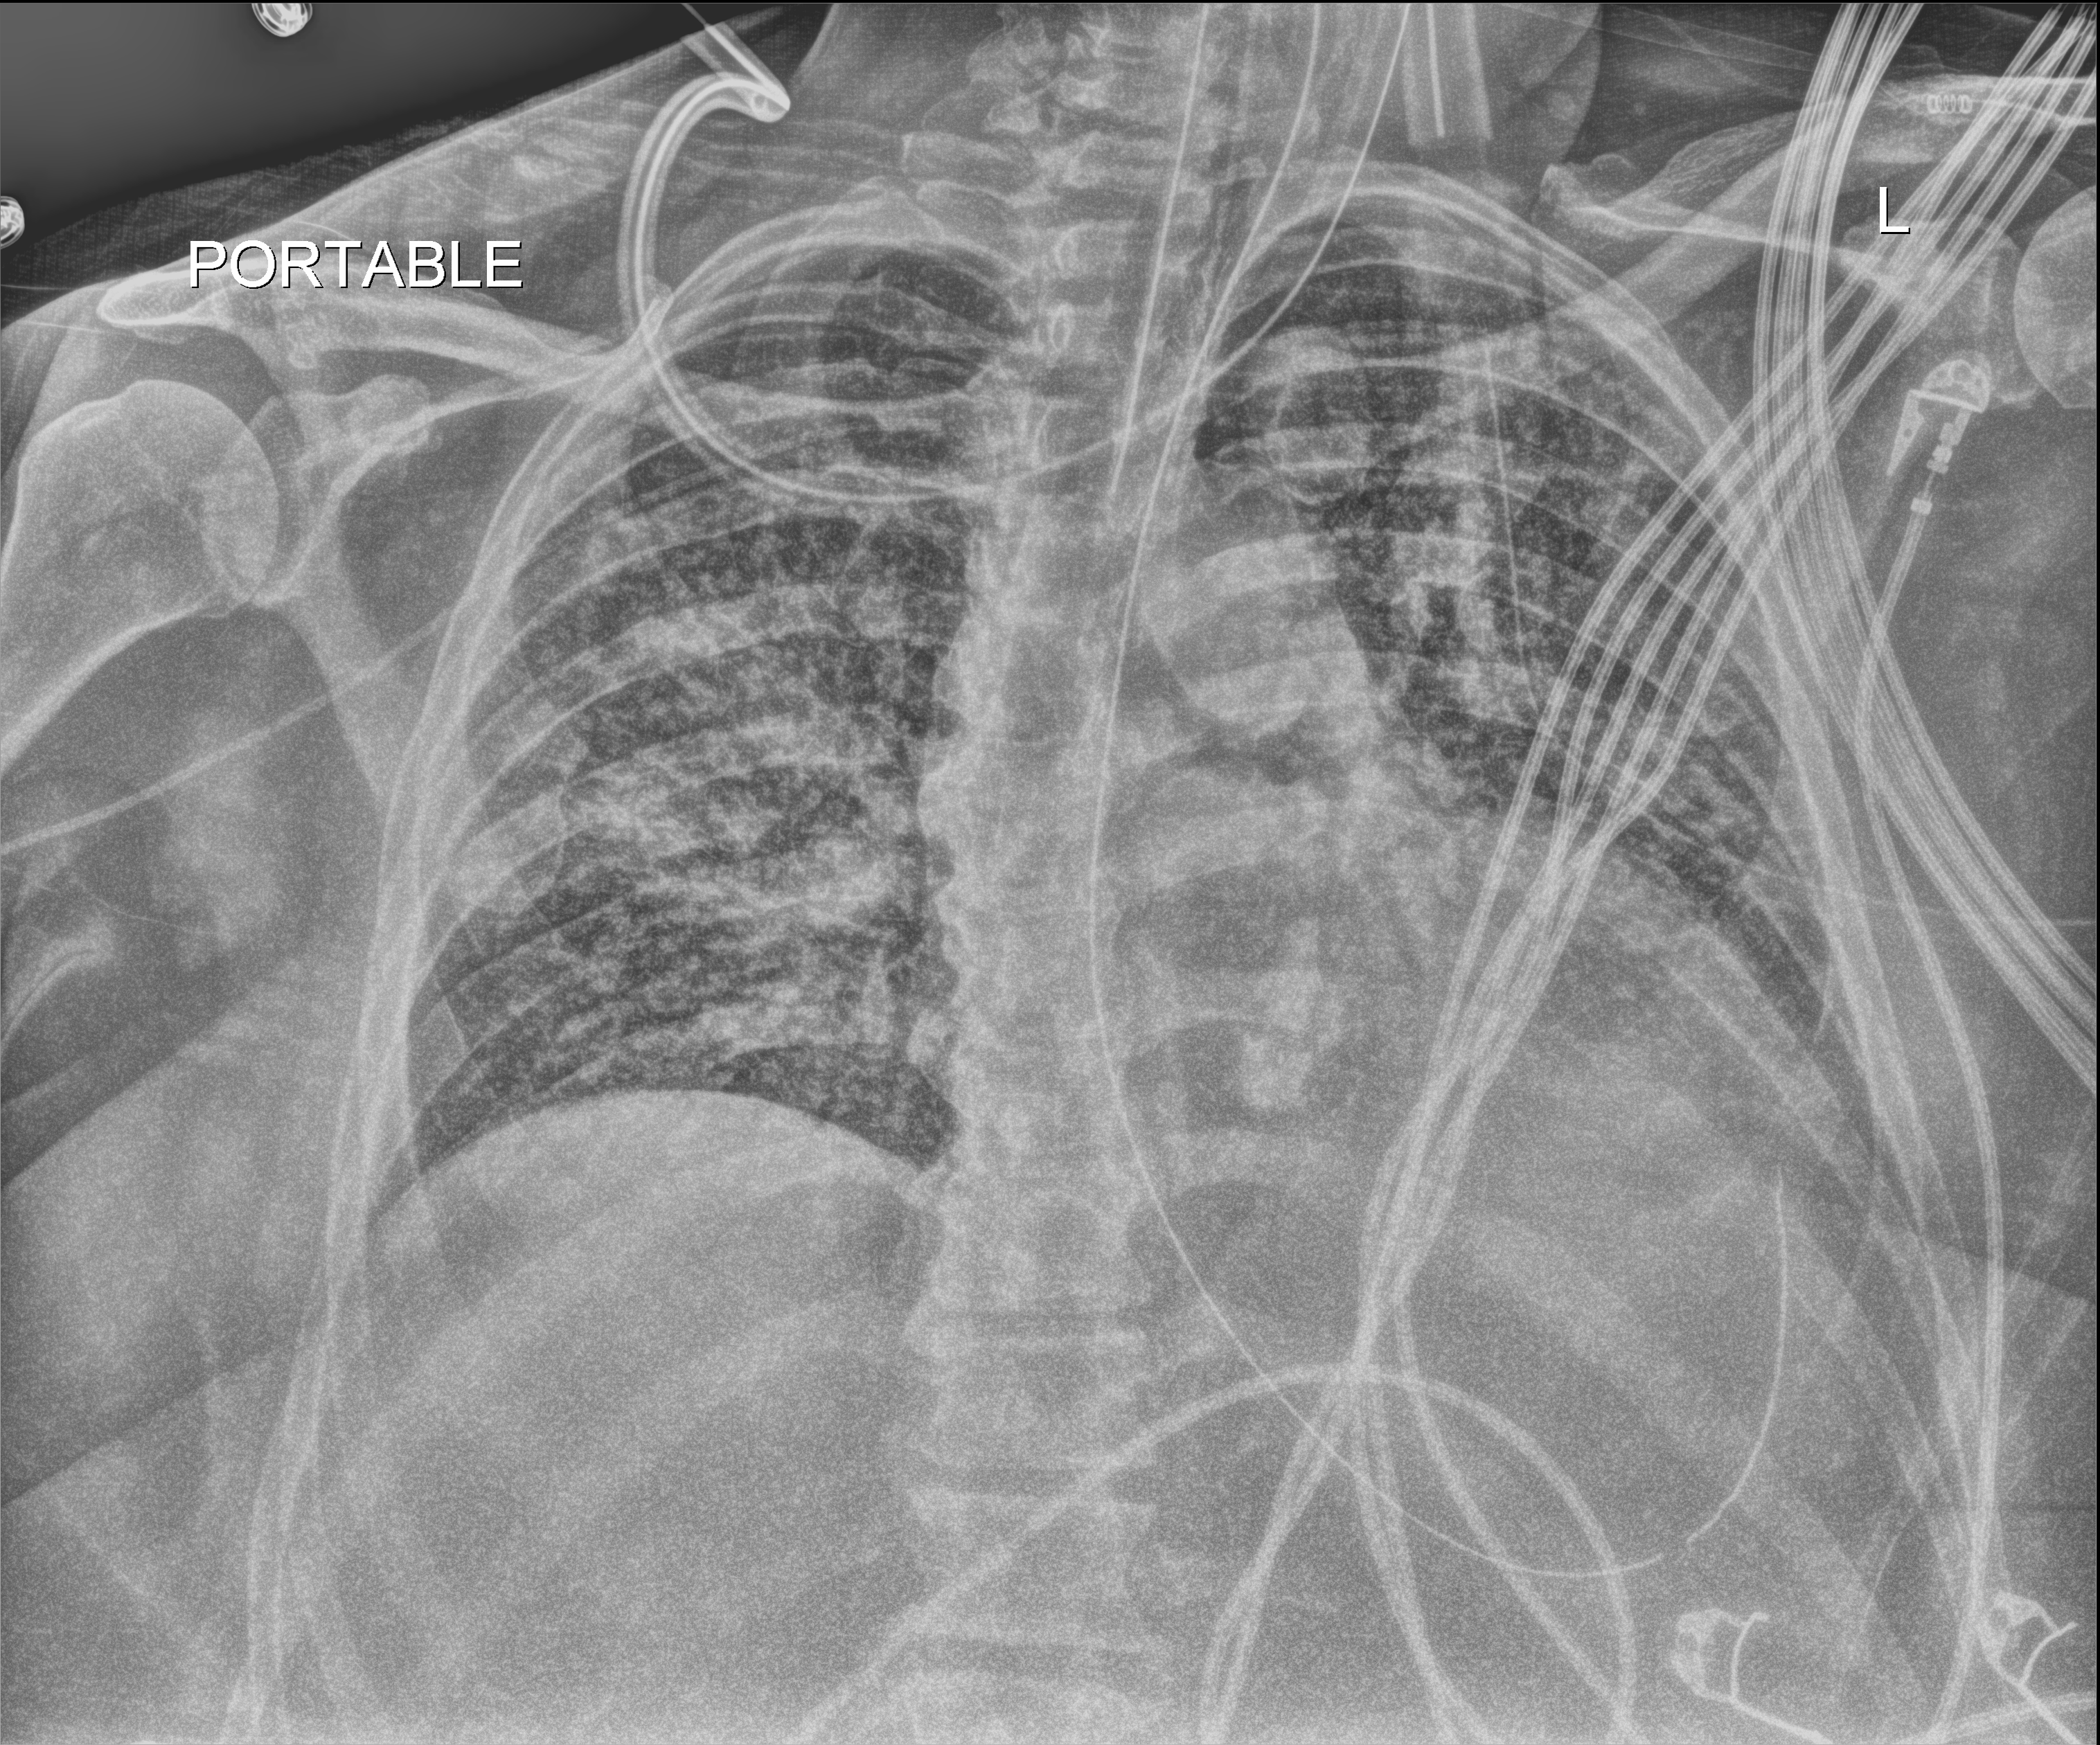
Chest radiograph, anteroposterior (AP) projection. Patient hospitalised with COVID-19, aged 18–59 years.
Admission-level facts for this patient (not findings on this image; timing relative to this image not recorded): admitted to intensive care during this hospital stay: yes; length of hospital stay: 28 days; mechanically ventilated during this hospital stay: yes.